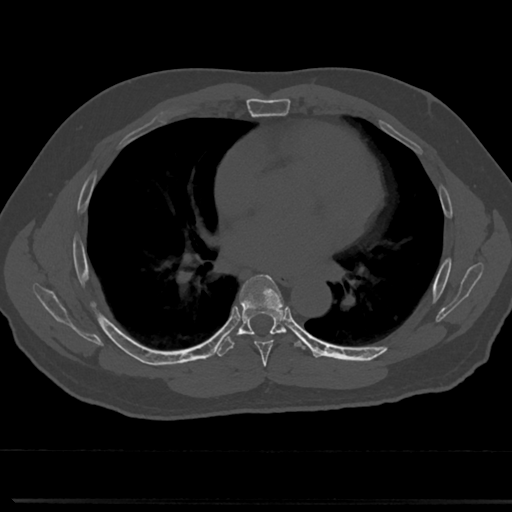
CT including the spine, one axial slice; slice 426 of 817 in the series (ordered by position); reconstruction kernel Br40s/3; 120 kVp; bone window (W 1800 / L 400 HU); 0.5 mm slice thickness; 512 × 512 image matrix, field of view 355 × 355 mm. Male patient, age 61 years. Case-level facts recorded for this patient, not image findings: primary cancer: prostate.
Outlined on this slice (semi-automatic segmentation, software-assisted and operator-edited):
- T5 vertebra: box from (x=266, y=372) to (x=269, y=375) px
- T6 vertebra: (x=239, y=275)–(x=288, y=358)
- T7 vertebra: (x=240, y=325)–(x=285, y=335)